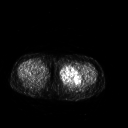
FDG PET of an extremity soft-tissue mass (from a PET/CT study), one axial slice; slice 232 of 267 in the series (ordered by position); 3.27 mm slice thickness; 128 × 128 image matrix. Female patient, age 42 years. From the clinical record (not read from this slice): histological type: pleiomorphic leiomyosarcoma; grade: intermediate; site of the primary tumour: left thigh.
Structures marked on this image (expert contour drawn on MRI and transferred to this co-registered scan by the dataset authors):
- gross tumour volume including surrounding oedema: bounding box <59,66,83,84> (left, top, right, bottom; pixels)
- gross tumour volume (mass): <59,66,81,84>